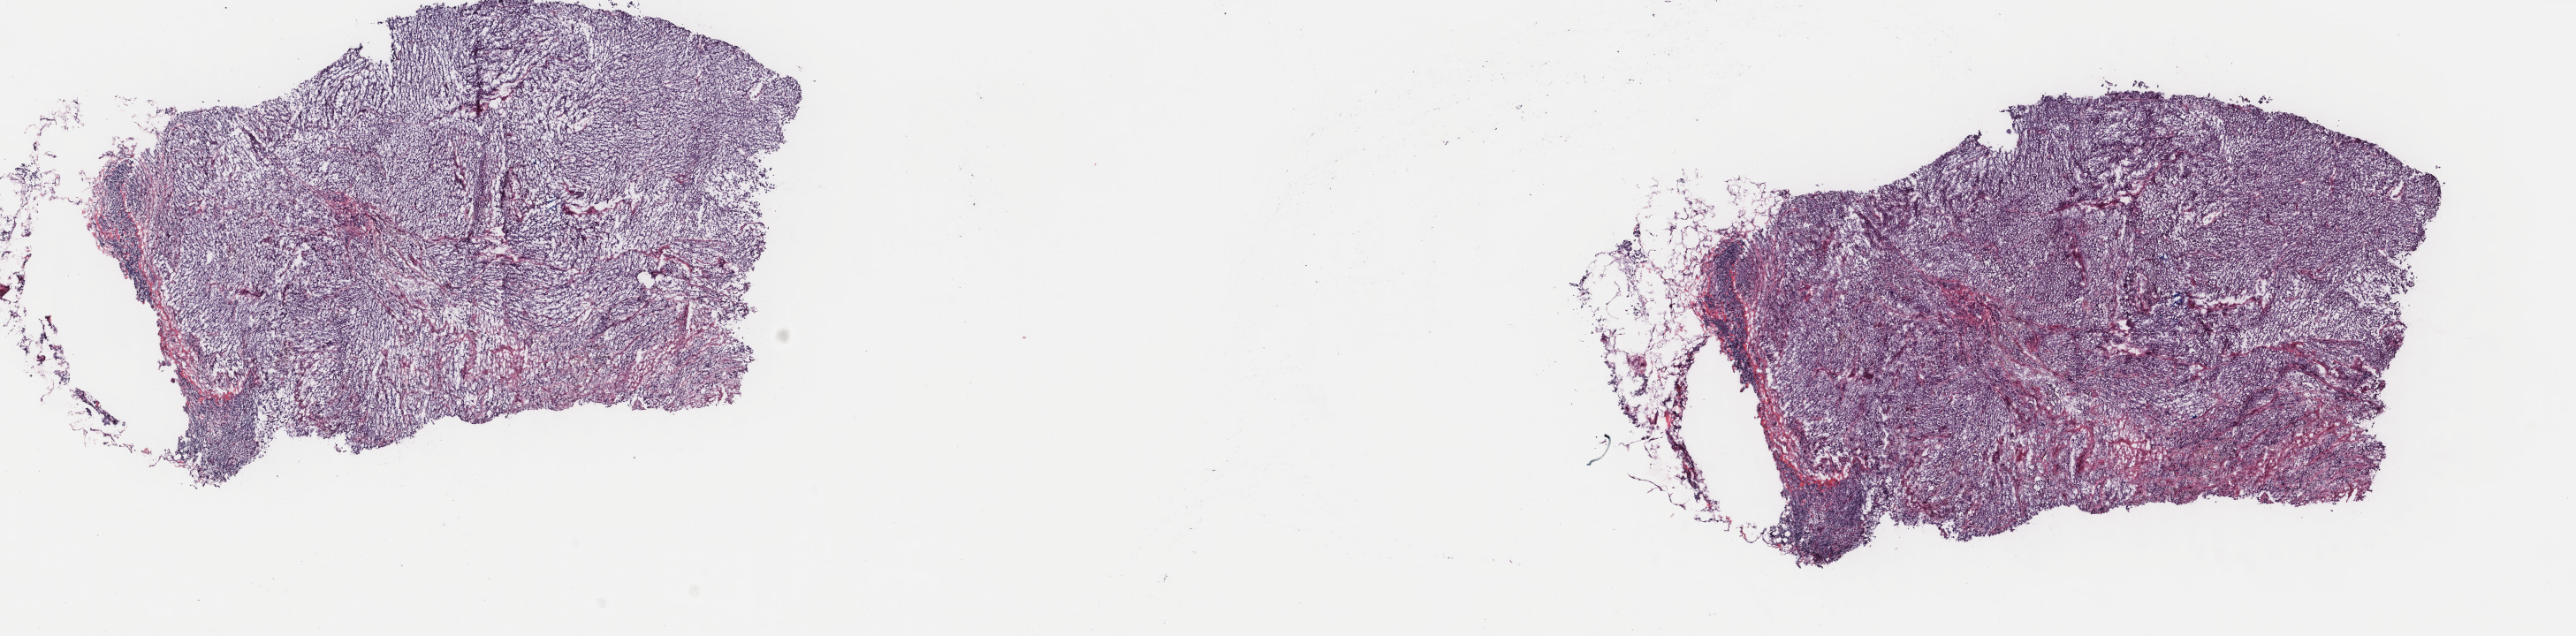
Whole-slide histology image, Hematoxylin and eosin (H&E) stained, whole scanned area (about 23.1 x 5.7 mm, from a 40x scan) shown as a low-resolution overview. Frozen section from the top of the tissue portion. Metastatic tumour sample, sampled site: lymph nodes of axilla or arm. Female, age 39 years at initial diagnosis. Pathologist review of this section (percent, as recorded): tumour cells 95%, tumour nuclei 80%, normal cells 0%, stromal cells 0%, necrosis 5%. Infiltration values recorded for this section: lymphocyte infiltration 5%, monocyte infiltration 3%, neutrophil infiltration 0%.
This section: metastatic tumour tissue. Patient diagnosis: Malignant melanoma, NOS.